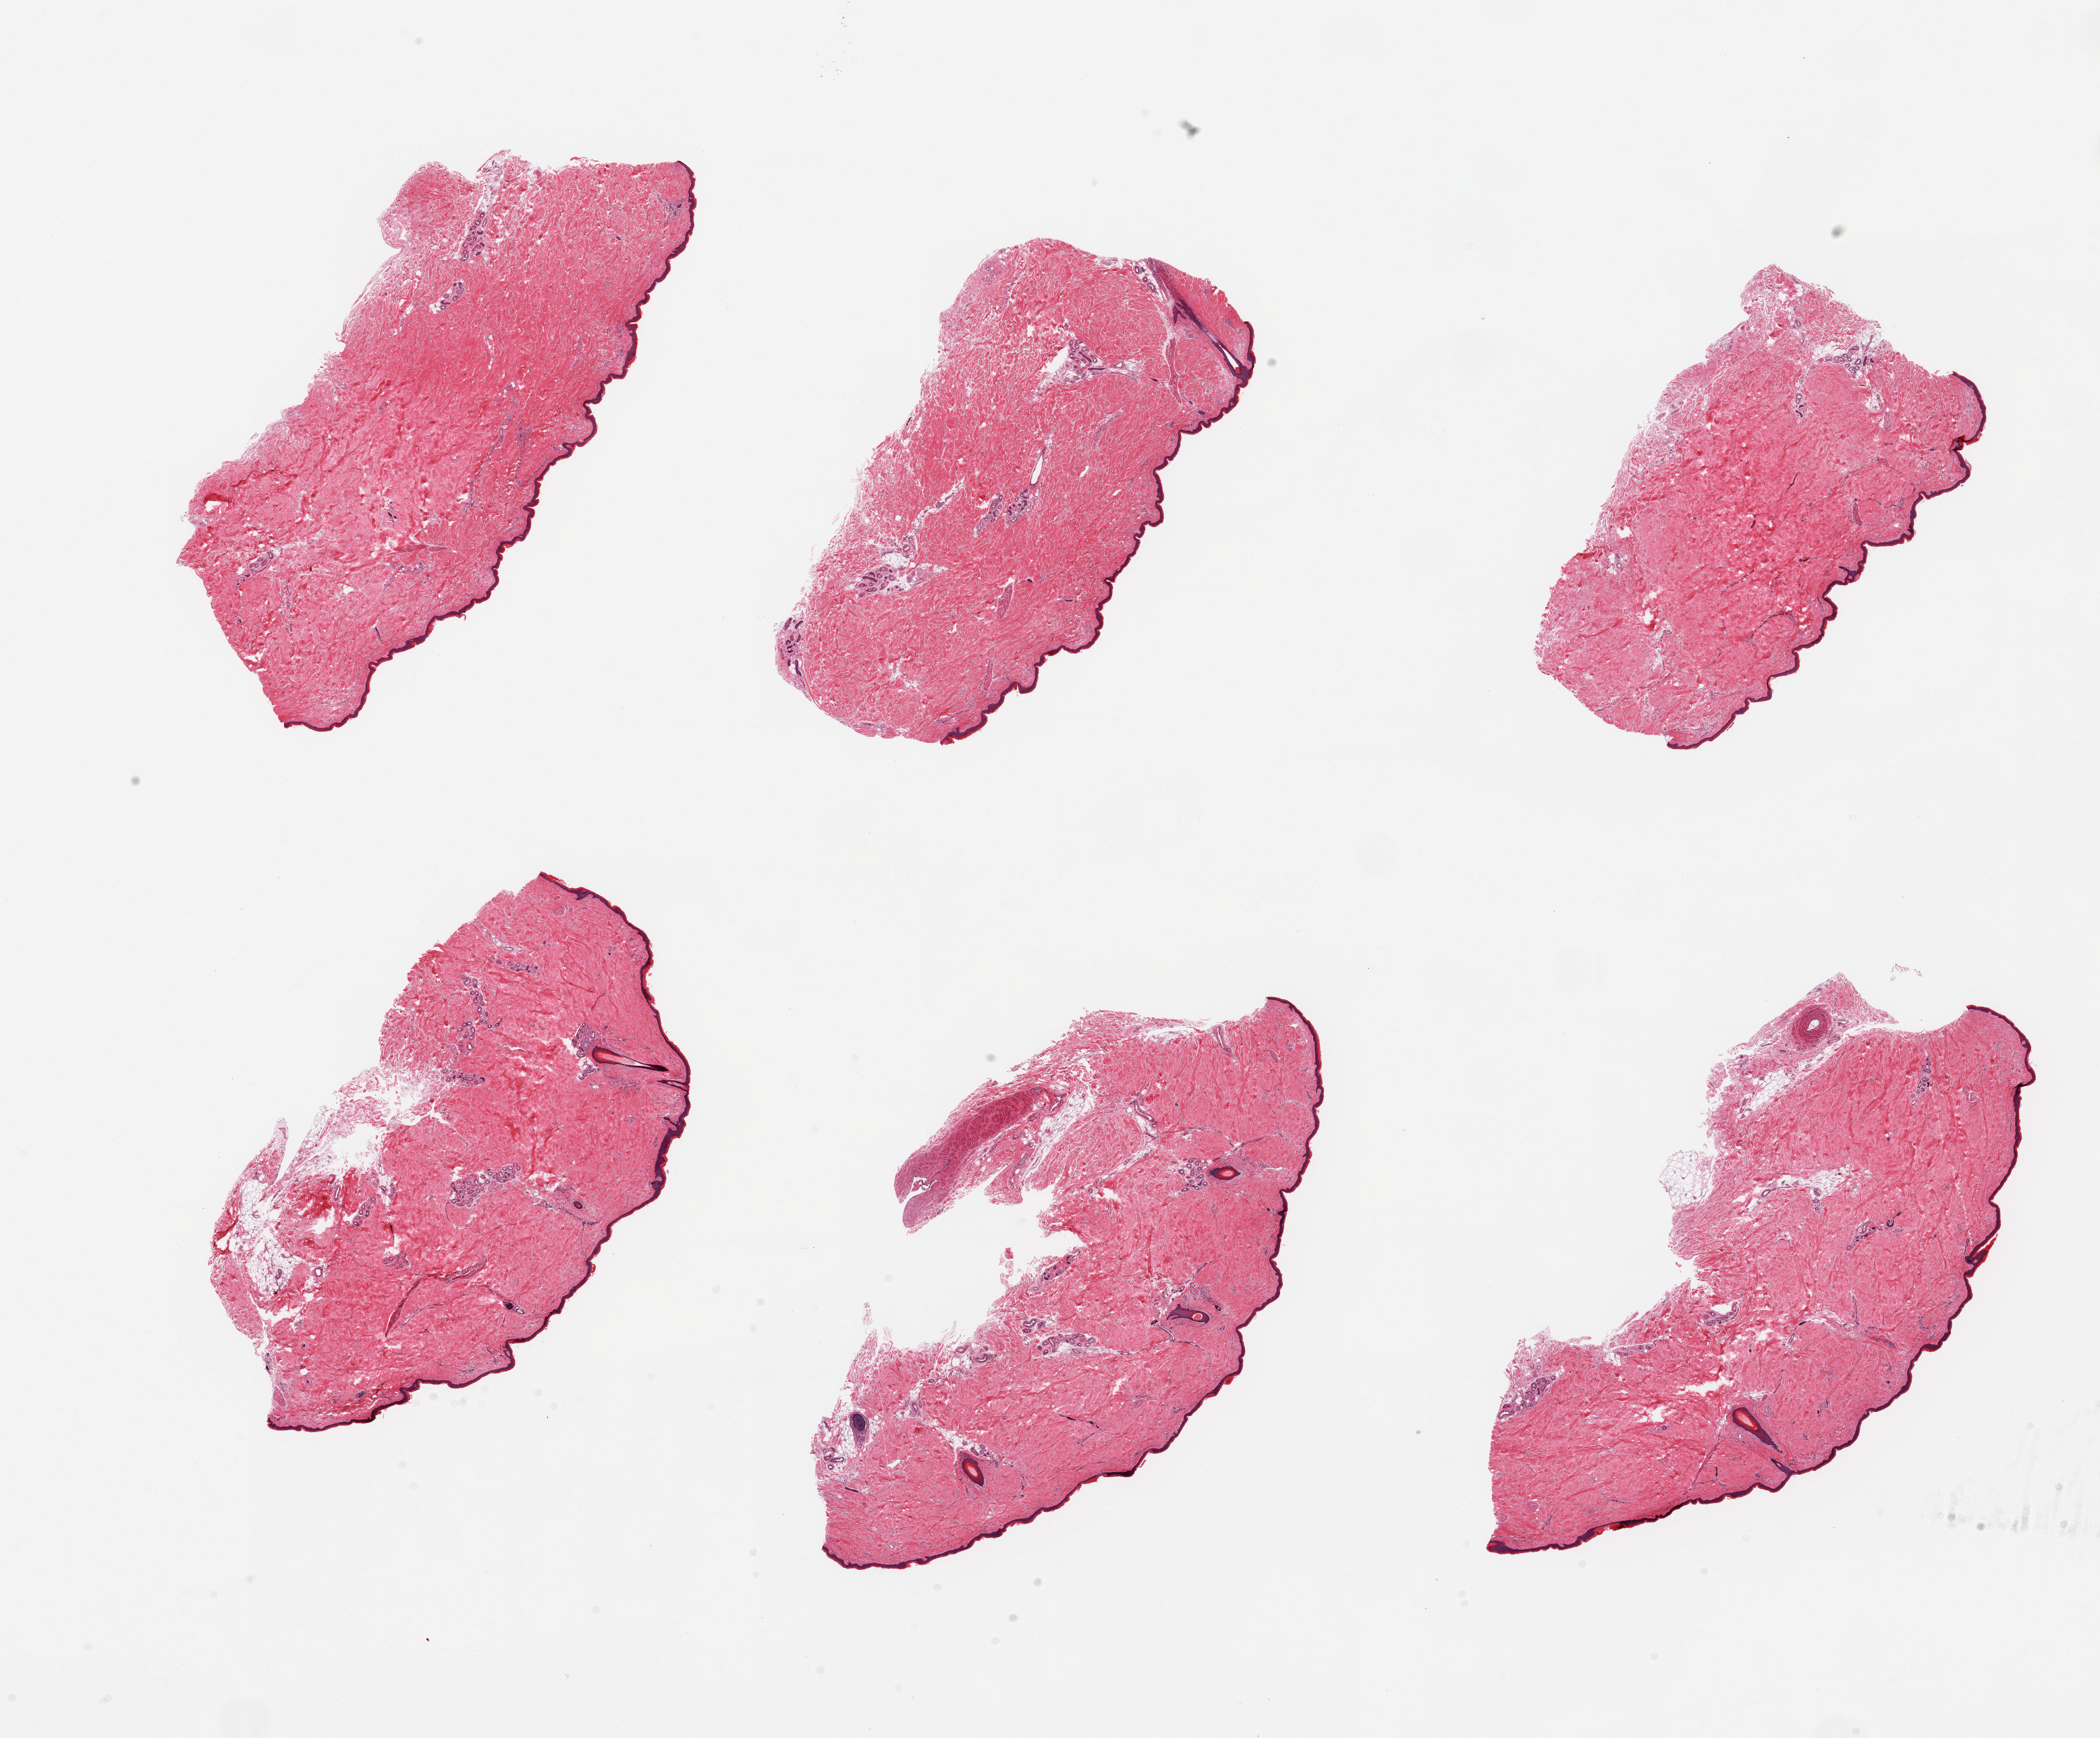
Whole-slide image, hematoxylin and eosin (H&E) stain — a low-resolution overview of the entire scanned area, about 24.6 x 20.4 mm (from a 20x scan); PAXgene-fixed paraffin-embedded (PFPE) section; sampled site (target tissue): skin of lower leg; tissue donor sample. Donor: male.
Reviewer comment on this tissue sample: 6 pieces, trace adherent dermal fat; squamous epithelium is ~30-40 microns.